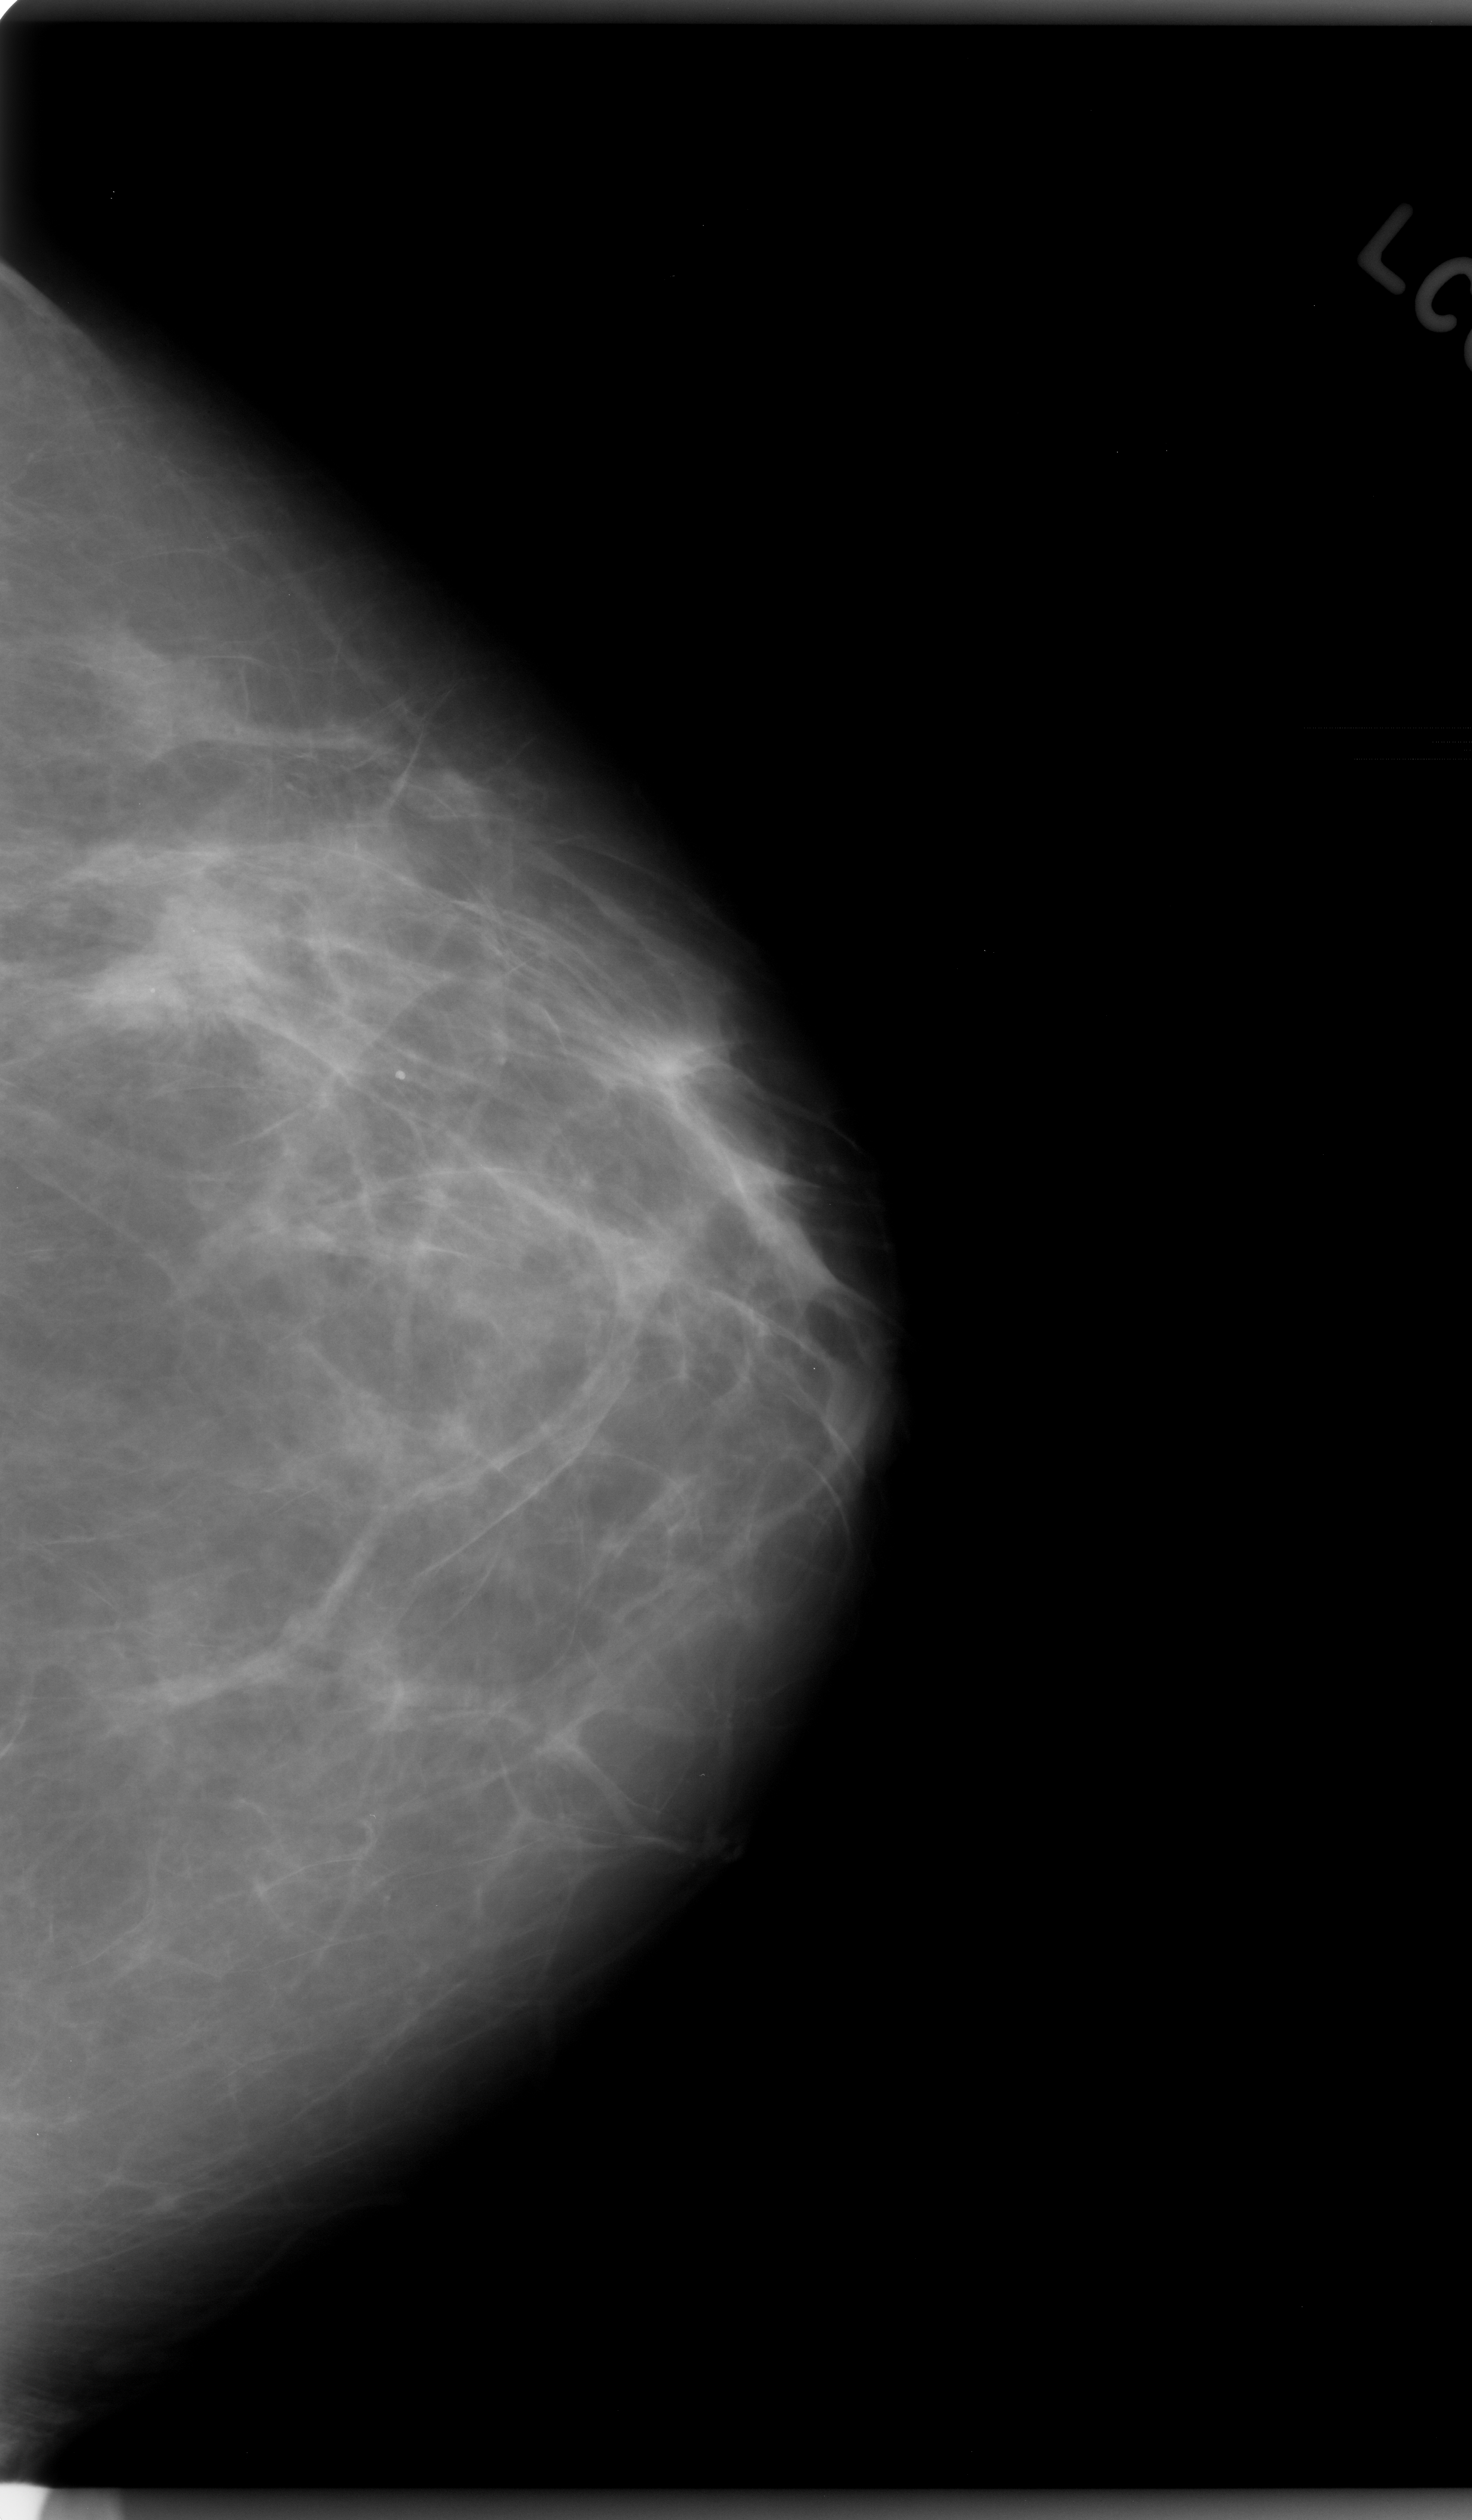
Scanned film-screen mammogram. Left breast. Craniocaudal (CC) view. 1472 × 2520 image matrix.
Expert-marked regions of interest on this film, with their recorded descriptors:
- mass, shape irregular, margins ill defined; BI-RADS assessment category 5; subtlety rating 4 on a 1 (subtle) to 5 (obvious) scale; pathology (as recorded): malignant: bounding box (x1, y1, x2, y2) in pixels: (81, 900, 253, 1061)